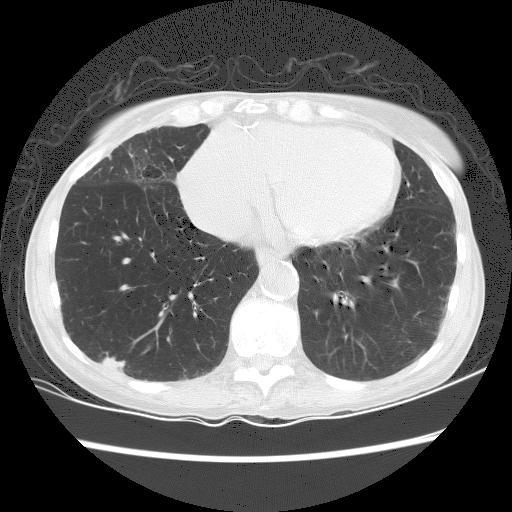
Low-dose screening chest CT, one axial slice; slice 61 of 156 in the series (ordered by position); 120 kVp; lung window (W 1500 / L -600 HU); 2.5 mm slice thickness; 512 × 512 image matrix, field of view 320 × 320 mm.
Annotated regions visible in this slice (manually delineated by an expert):
- lesion 1 (tumor, lower lobe of right lung): box from (x=101, y=352) to (x=126, y=372) px